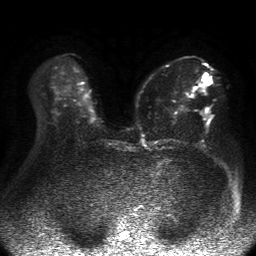
Breast MRI, one axial slice. Position 30 of 50 along the scan axis. Diffusion-weighted series; image 2 of 4 stored at this slice position (different b-values; order by instance number). 1.5 T. 4 mm slice thickness. 256 × 256 image matrix, field of view 360 × 360 mm. Female patient.
Annotated regions visible in this slice (manually delineated by an expert):
- tumour on diffusion-weighted imaging: bounding box [x1, y1, x2, y2] px = [202, 112, 209, 120]